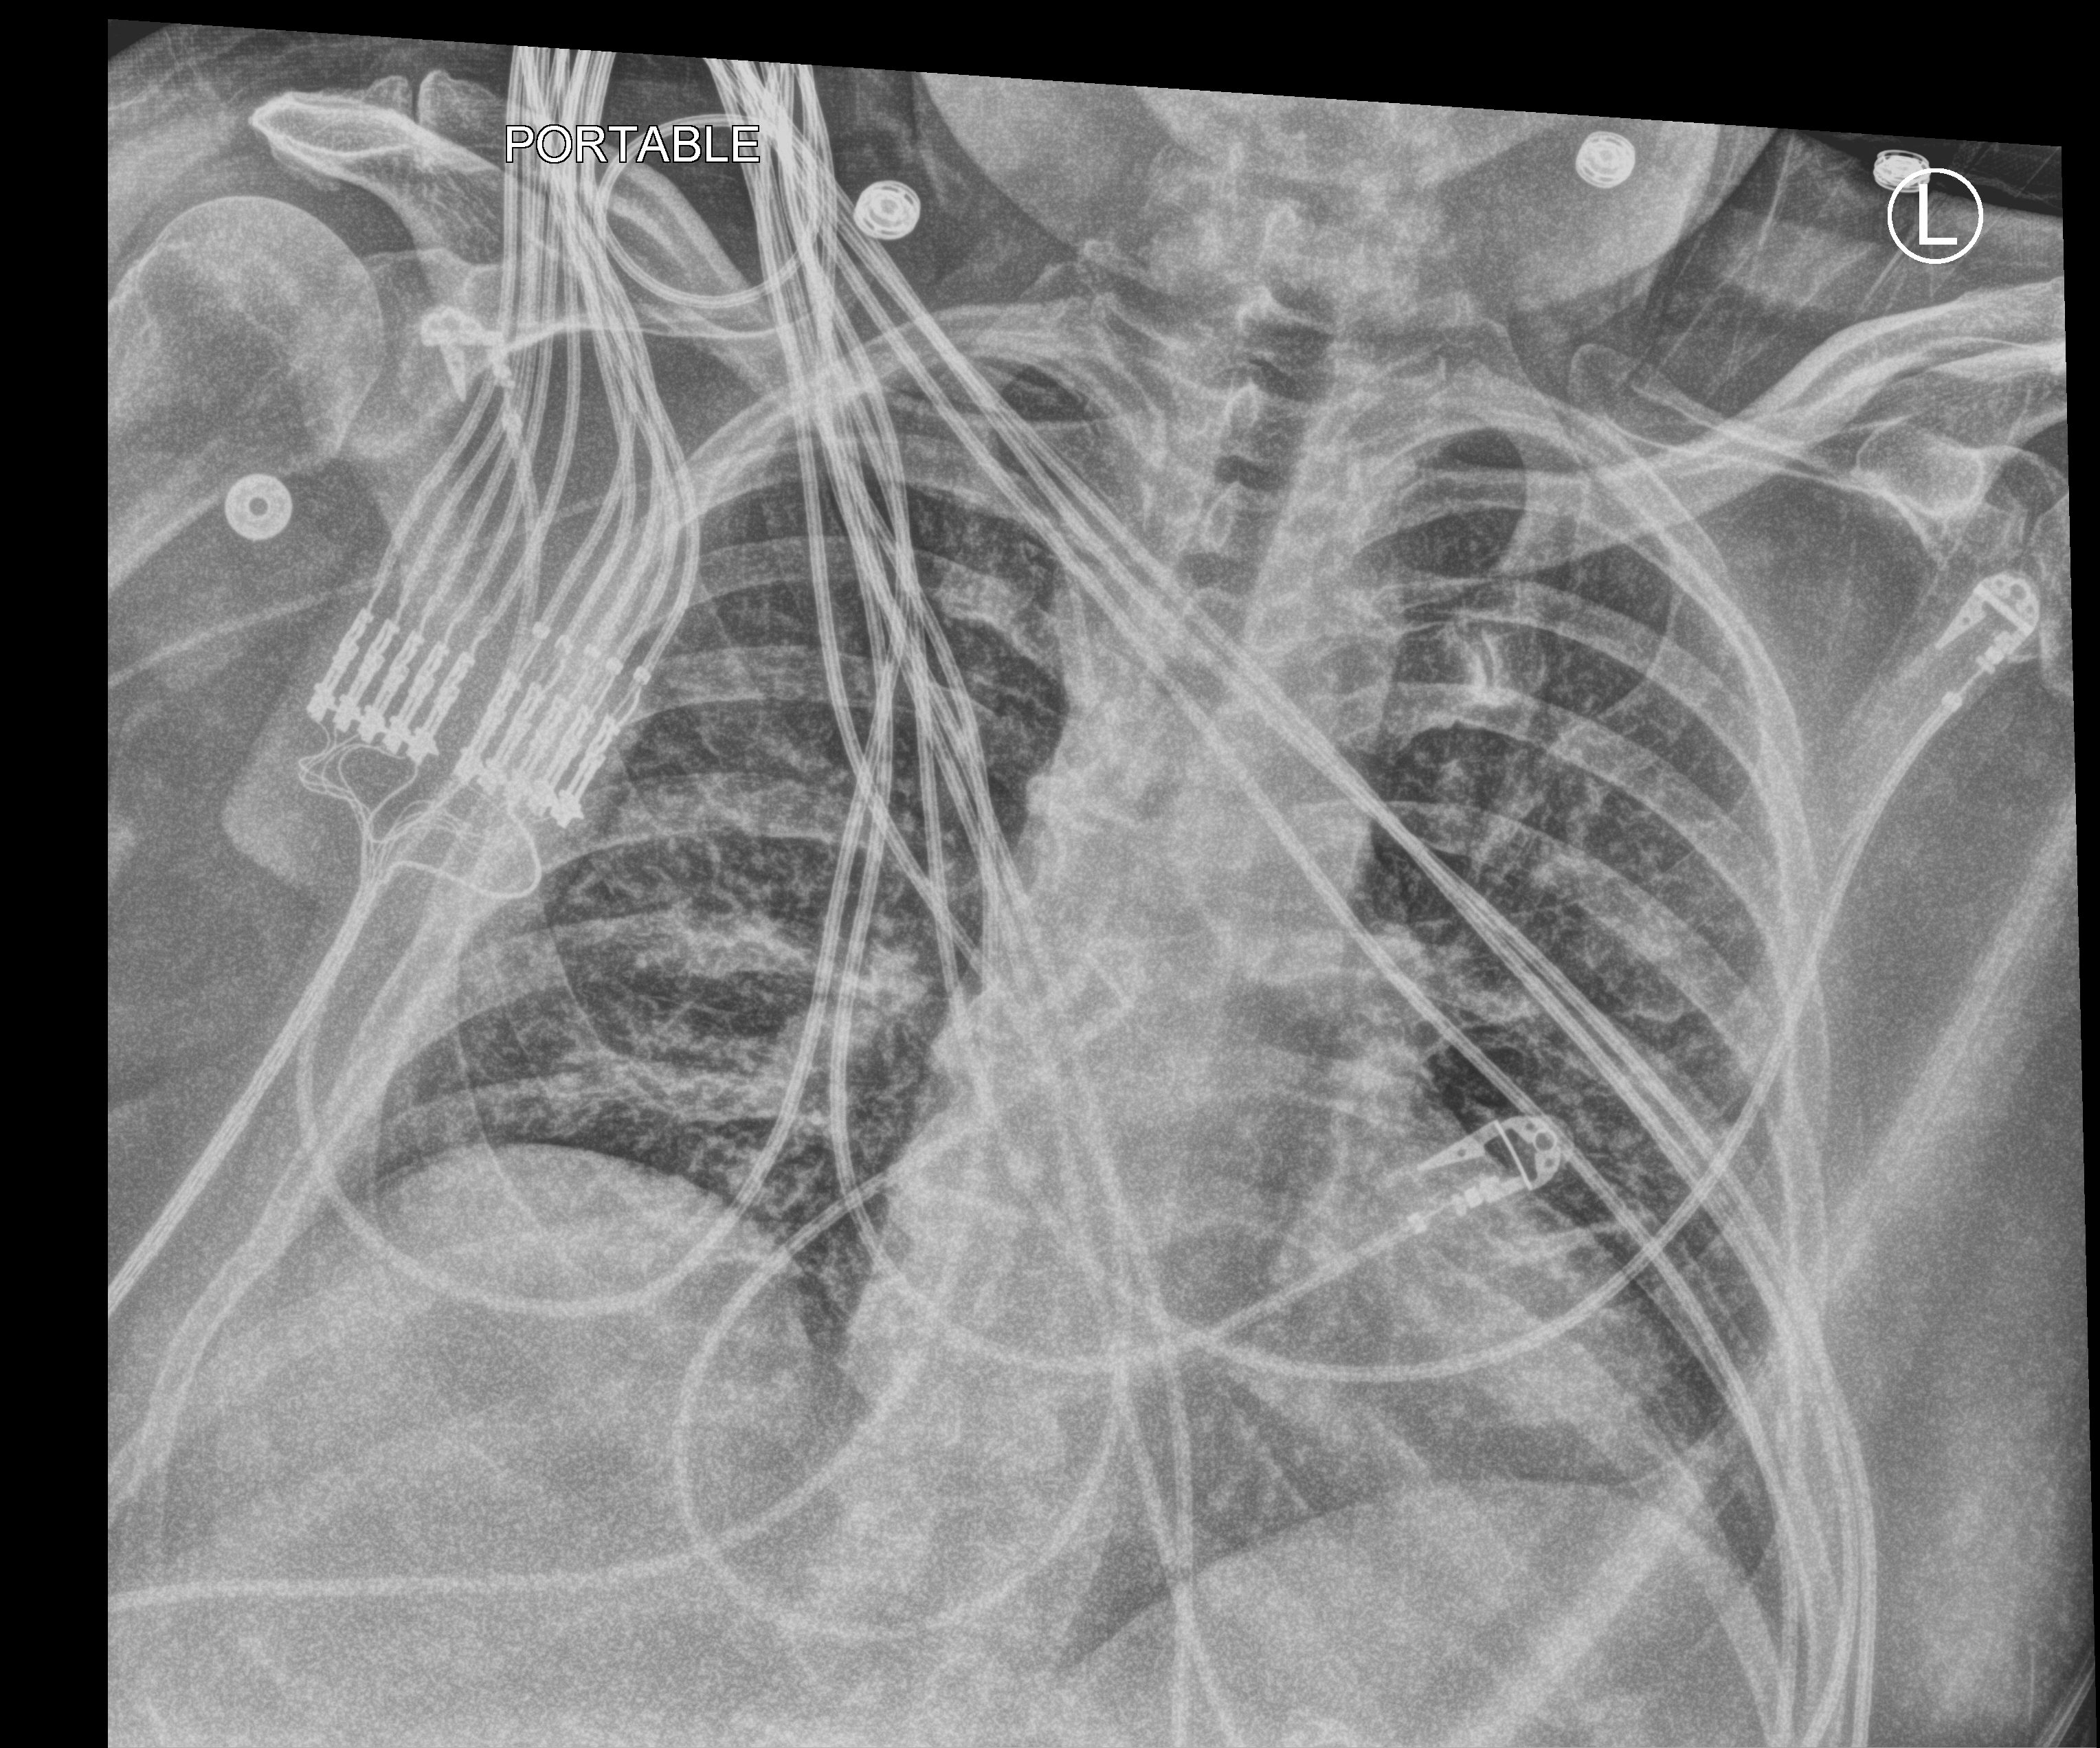
Bedside chest radiograph (computed radiography), anteroposterior (AP) projection. Male patient hospitalised with COVID-19, age 18–59 years.
Hospital-stay facts (about this admission, not read from this image; timing relative to this image not recorded): admitted to intensive care during this hospital stay: yes; length of hospital stay: 21 days.